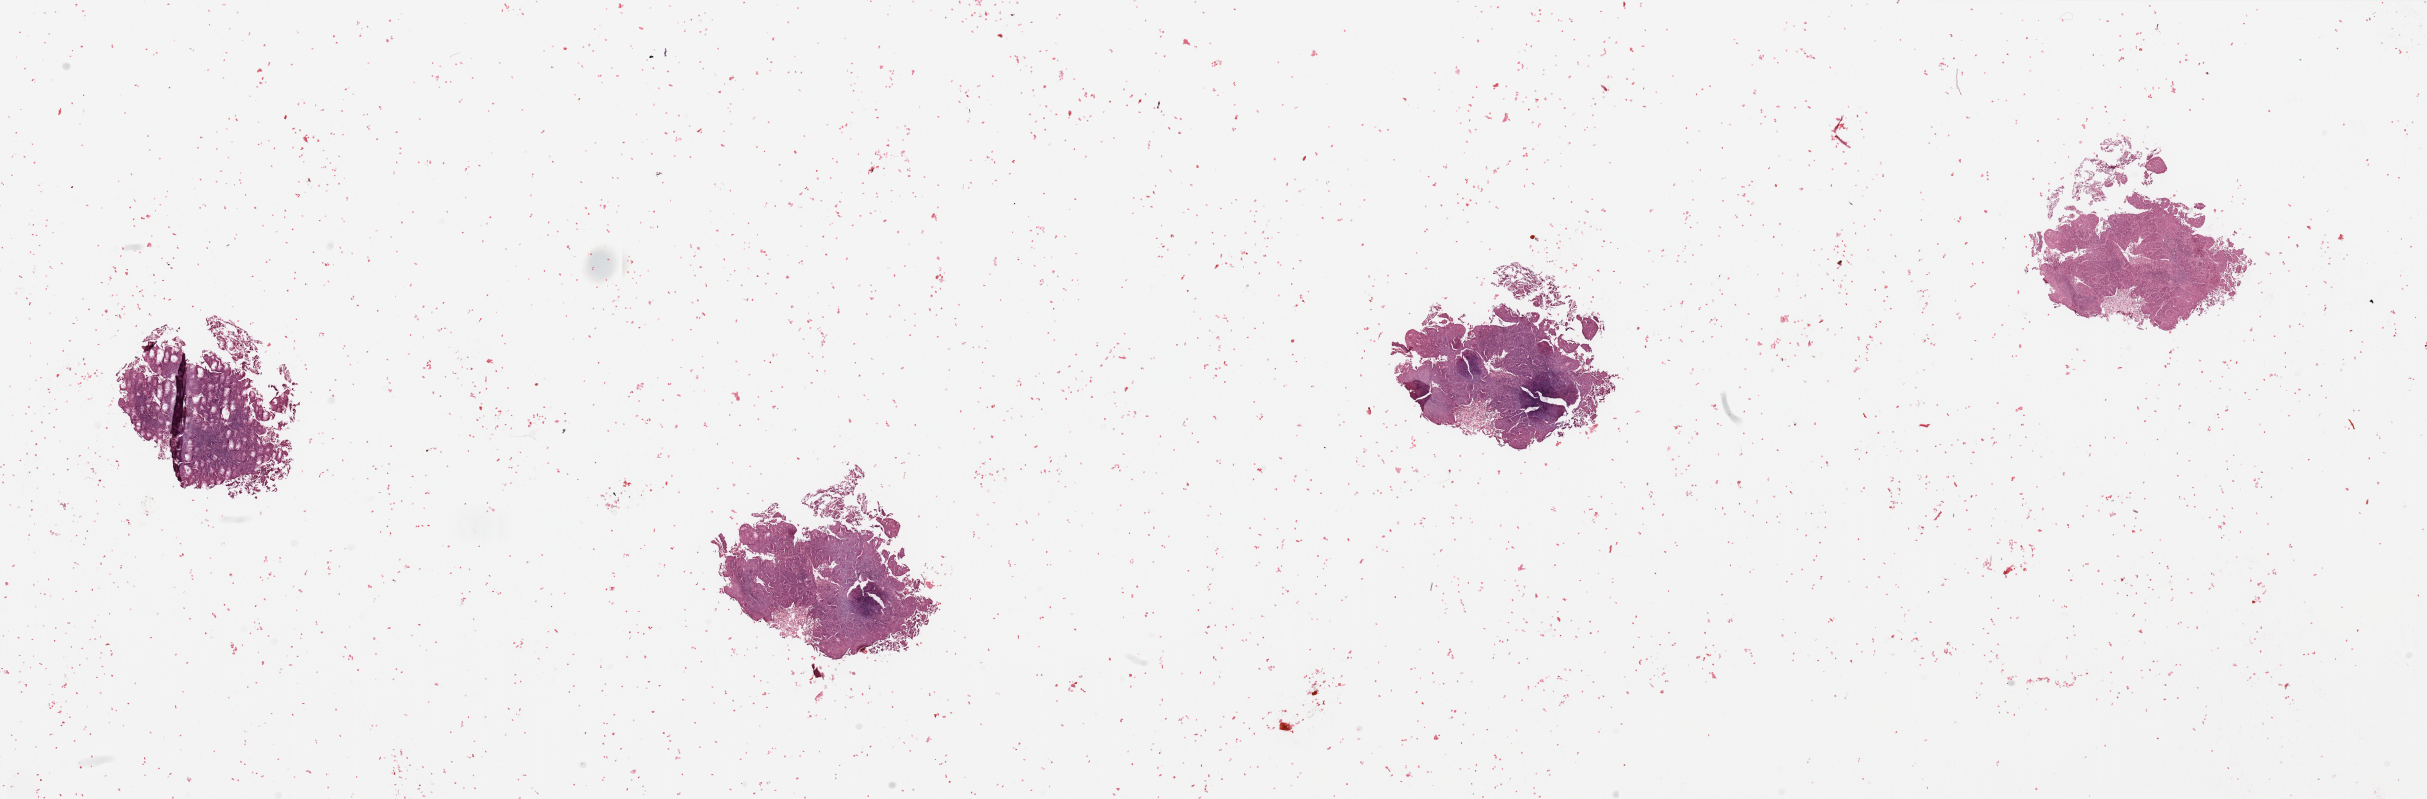
Digitized H&E-stained tissue section (whole slide) — a low-resolution overview of the entire scanned area, about 38.4 x 12.6 mm; tumour tissue sample, sampled site: uterus. 82-year-old female patient. Histologic grade: G2 (moderately differentiated). Pathologist review of this section (percent, as recorded): tumour nuclei 80%, necrosis 3%.
Primary tumour site (as recorded): anterior endometrium. Histologic diagnosis: Endometrioid adenocarcinoma, NOS. AJCC pathologic stage: I.